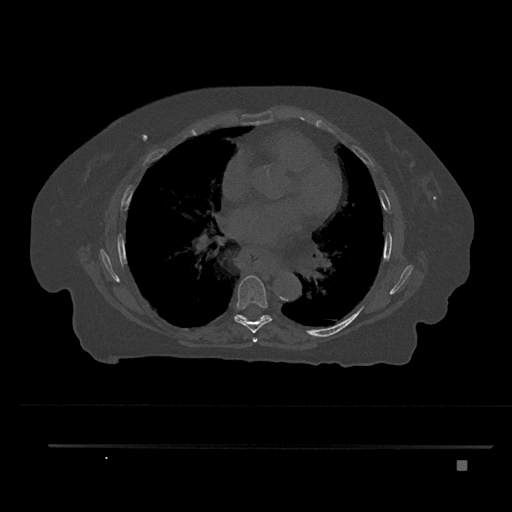
CT including the spine, one axial slice; position 480 of 797 along the scan axis; 120 kVp; bone window (W 1800 / L 400 HU); 0.5 mm slice thickness; 512 × 512 image matrix, field of view 437 × 437 mm. Patient: female, 76 years. Case-level facts recorded for this patient, not image findings: primary cancer: lung.
Outlined on this slice (semi-automatically segmented with operator editing):
- T6 vertebra: bounding box <252,337,258,343> (left, top, right, bottom; pixels)
- T7 vertebra: <234,275,272,333>
- T8 vertebra: <235,315,270,321>